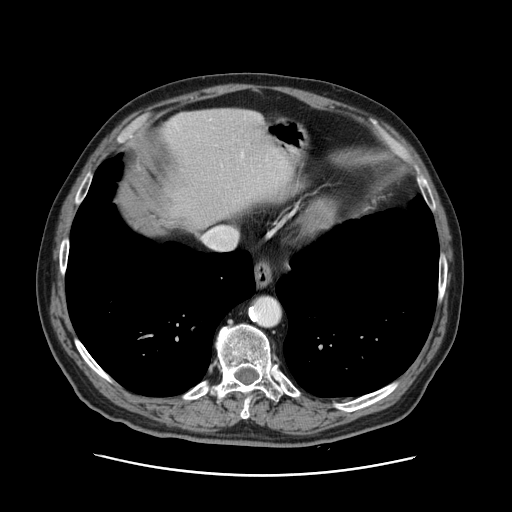
Contrast-enhanced abdominal CT, one axial slice. Slice 115 of 141 in the series (ordered by position). 120 kVp. Soft-tissue window (W 400 / L 40 HU). 2.5 mm slice thickness. 512 × 512 image matrix. Male patient, age 72 years. From the clinical record (not read from this slice): diagnosis: colorectal cancer liver metastases, imaged before liver resection; multiple liver metastases: yes; largest metastasis: 5.4 cm; disease in both lobes: yes.
Outlined on this slice (outlined manually by an expert reader):
- liver: bounding box (x1, y1, x2, y2) in pixels: (161, 108, 286, 229)
- planned liver remnant (the part of the liver to remain after resection): (162, 108, 289, 228)